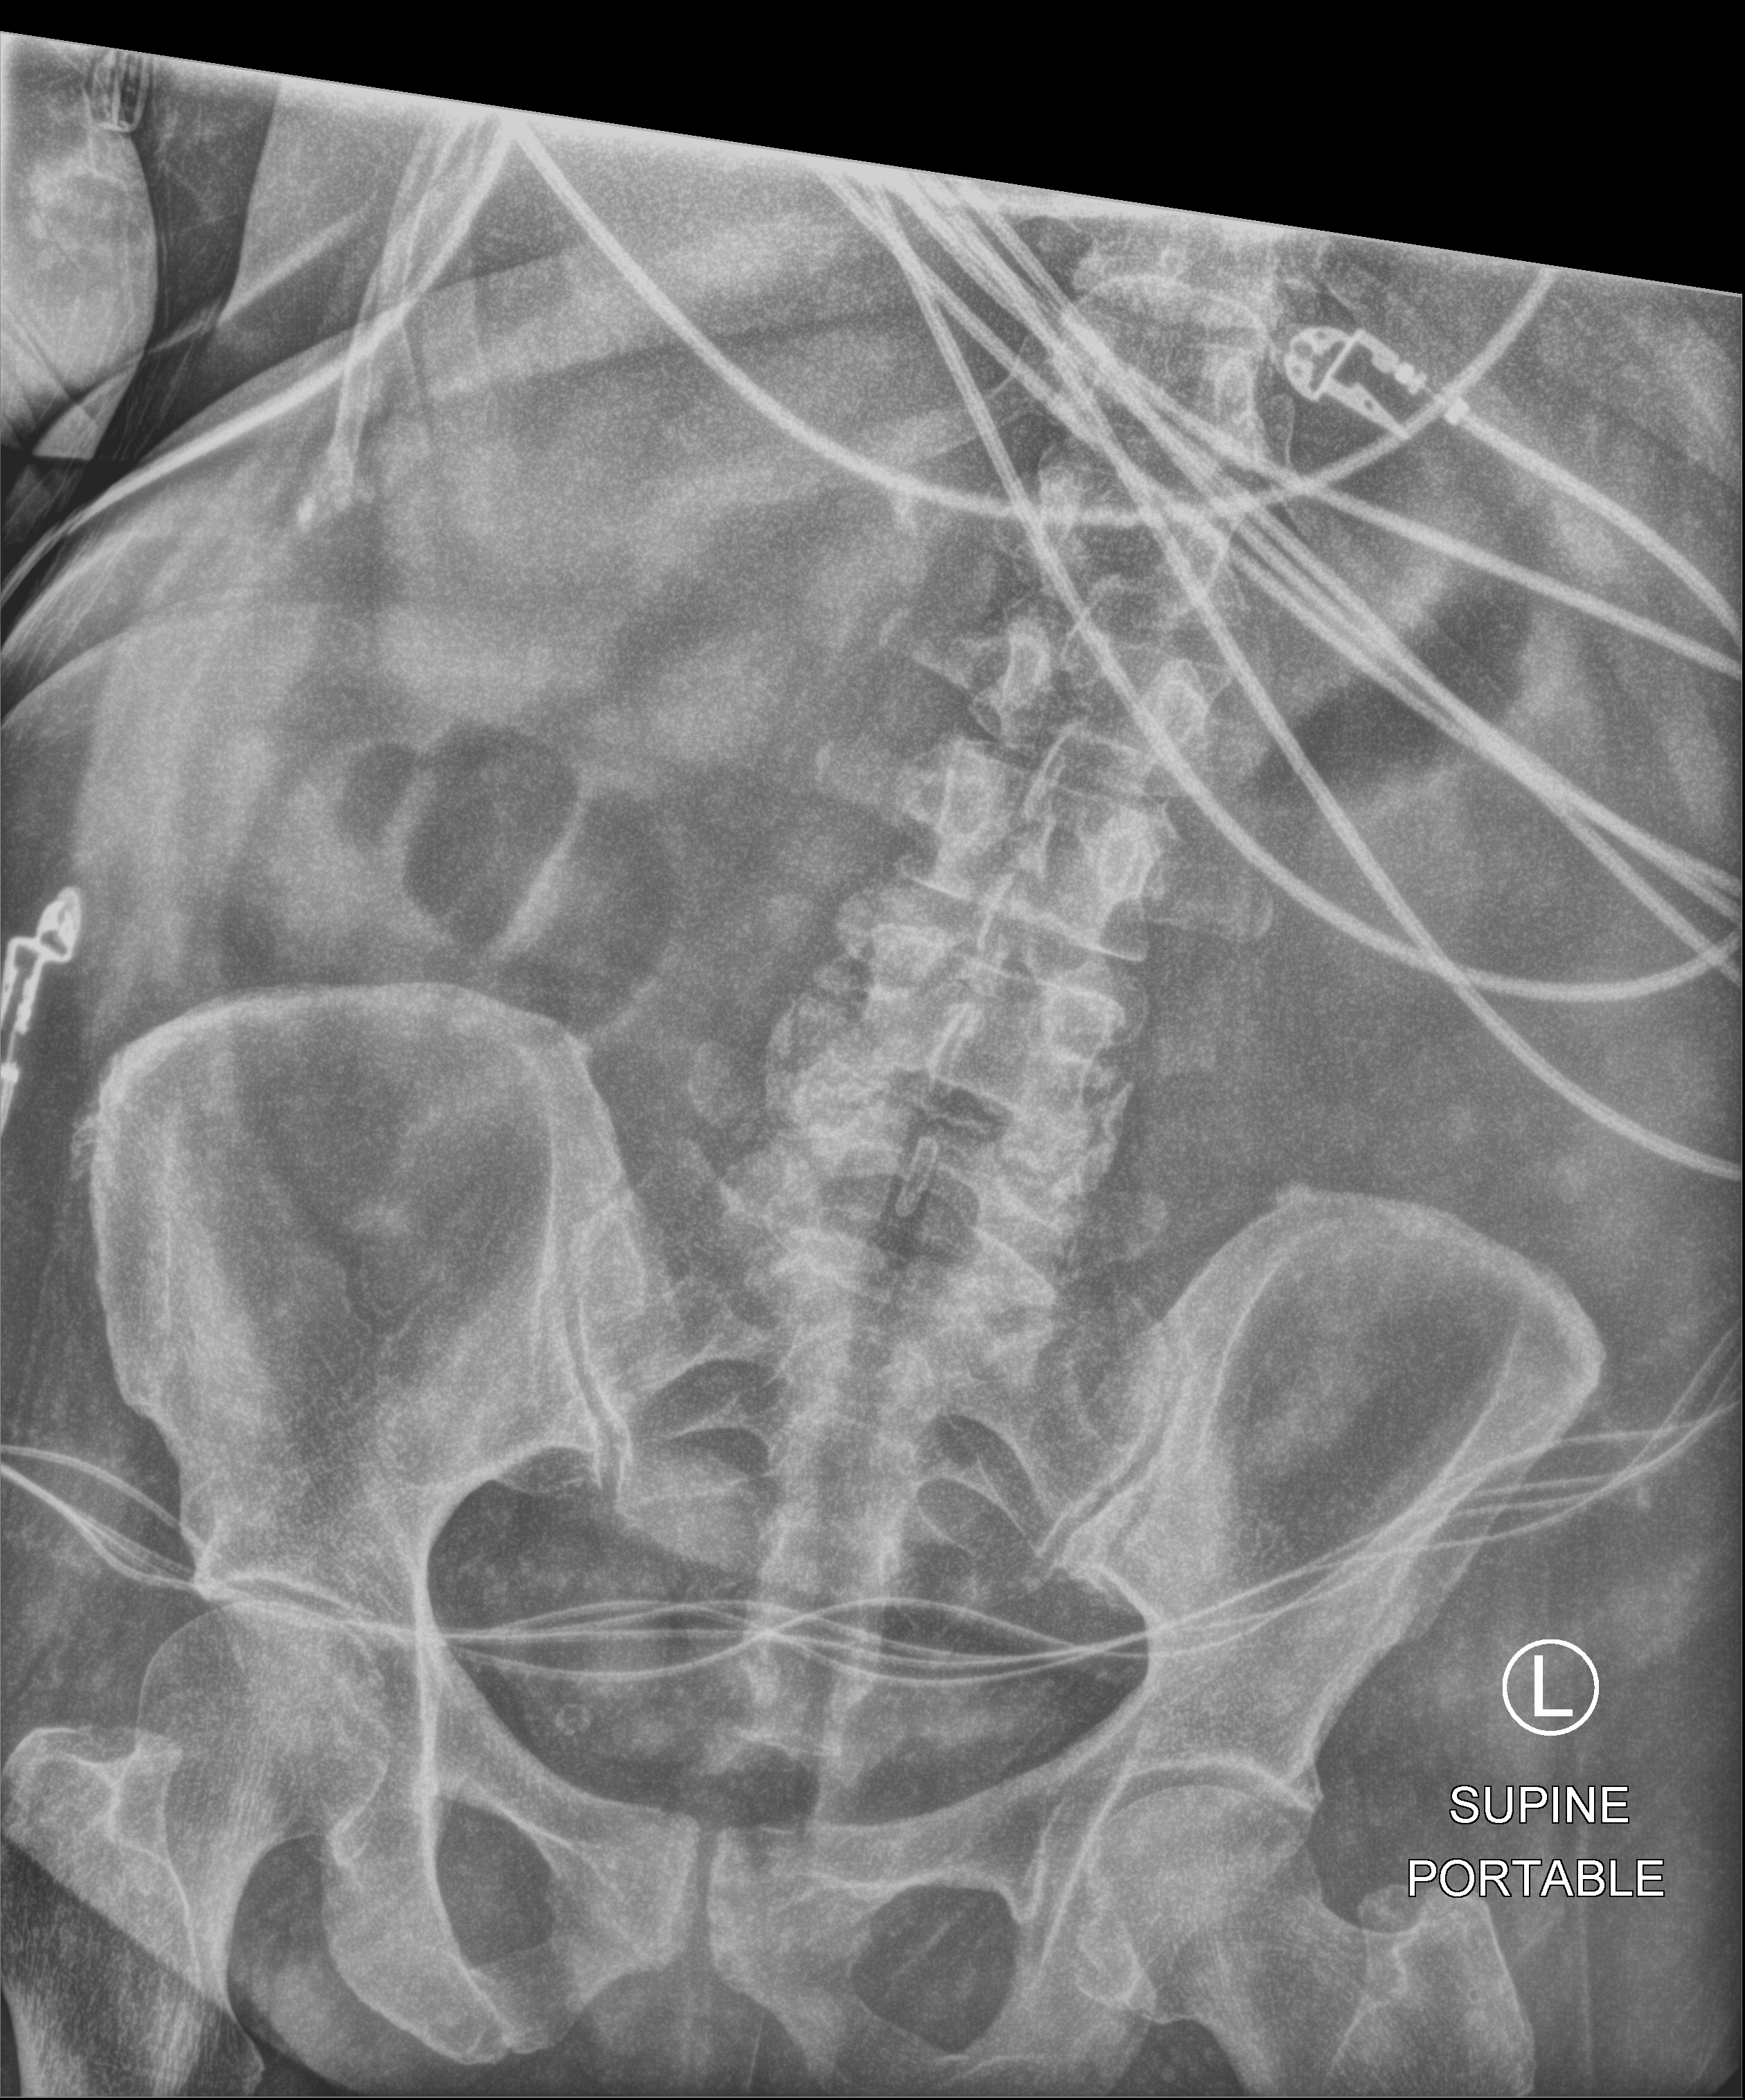
Portable abdomen radiograph, anteroposterior (AP) projection. Female patient hospitalised with COVID-19, age 60–74 years.
From the hospital-stay record, not from the radiograph (when in the stay this image was taken is not recorded): COPD (admission record): no; chronic kidney disease (admission record): no; admitted to intensive care during this hospital stay: yes.